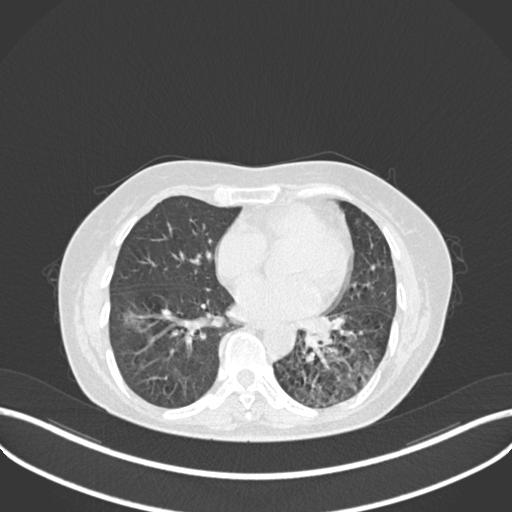
Chest CT, one axial slice; position 108 of 270 along the scan axis; 120 kVp; lung window (W 1500 / L -600 HU); 1 mm slice thickness; 512 × 512 image matrix, field of view 400 × 400 mm. Patient: female, 63 years. Case-level facts recorded for this patient, not image findings: clinical TNM (as recorded): T1b N0 M0.
Annotated regions visible in this slice (rectangle marked by the reading radiologist):
- lung tumour (recorded histology: adenocarcinoma): bounding box [x1, y1, x2, y2] px = [294, 307, 337, 355]